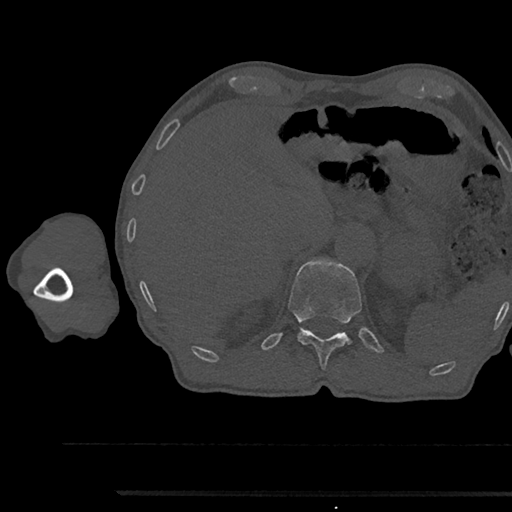
CT including the spine, one axial slice. Position 708 of 797 along the scan axis. Bone window (W 1800 / L 400 HU). 0.5 mm slice thickness. 512 × 512 image matrix, field of view 367 × 367 mm. Male patient, age 79 years. Case-level facts recorded for this patient, not image findings: primary cancer: prostate.
Annotated regions visible in this slice (semi-automatic segmentation, software-assisted and operator-edited):
- T12 vertebra: bounding box (x1, y1, x2, y2) in pixels: (289, 259, 362, 370)